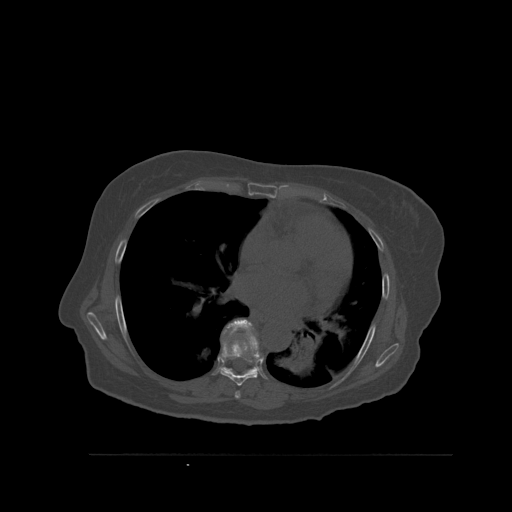
CT including the spine, one axial slice; bone window (W 1800 / L 400 HU); 1.5 mm slice thickness; 512 × 512 image matrix, field of view 470 × 470 mm. Female patient, age 73 years. Case-level facts recorded for this patient, not image findings: primary cancer: breast; vertebrae with lytic lesions (as recorded): L2.
Structures marked on this image (semi-automatically segmented with operator editing):
- T6 vertebra: bounding box [x1, y1, x2, y2] px = [235, 391, 240, 399]
- T7 vertebra: [220, 336, 262, 386]
- T8 vertebra: [222, 319, 257, 374]